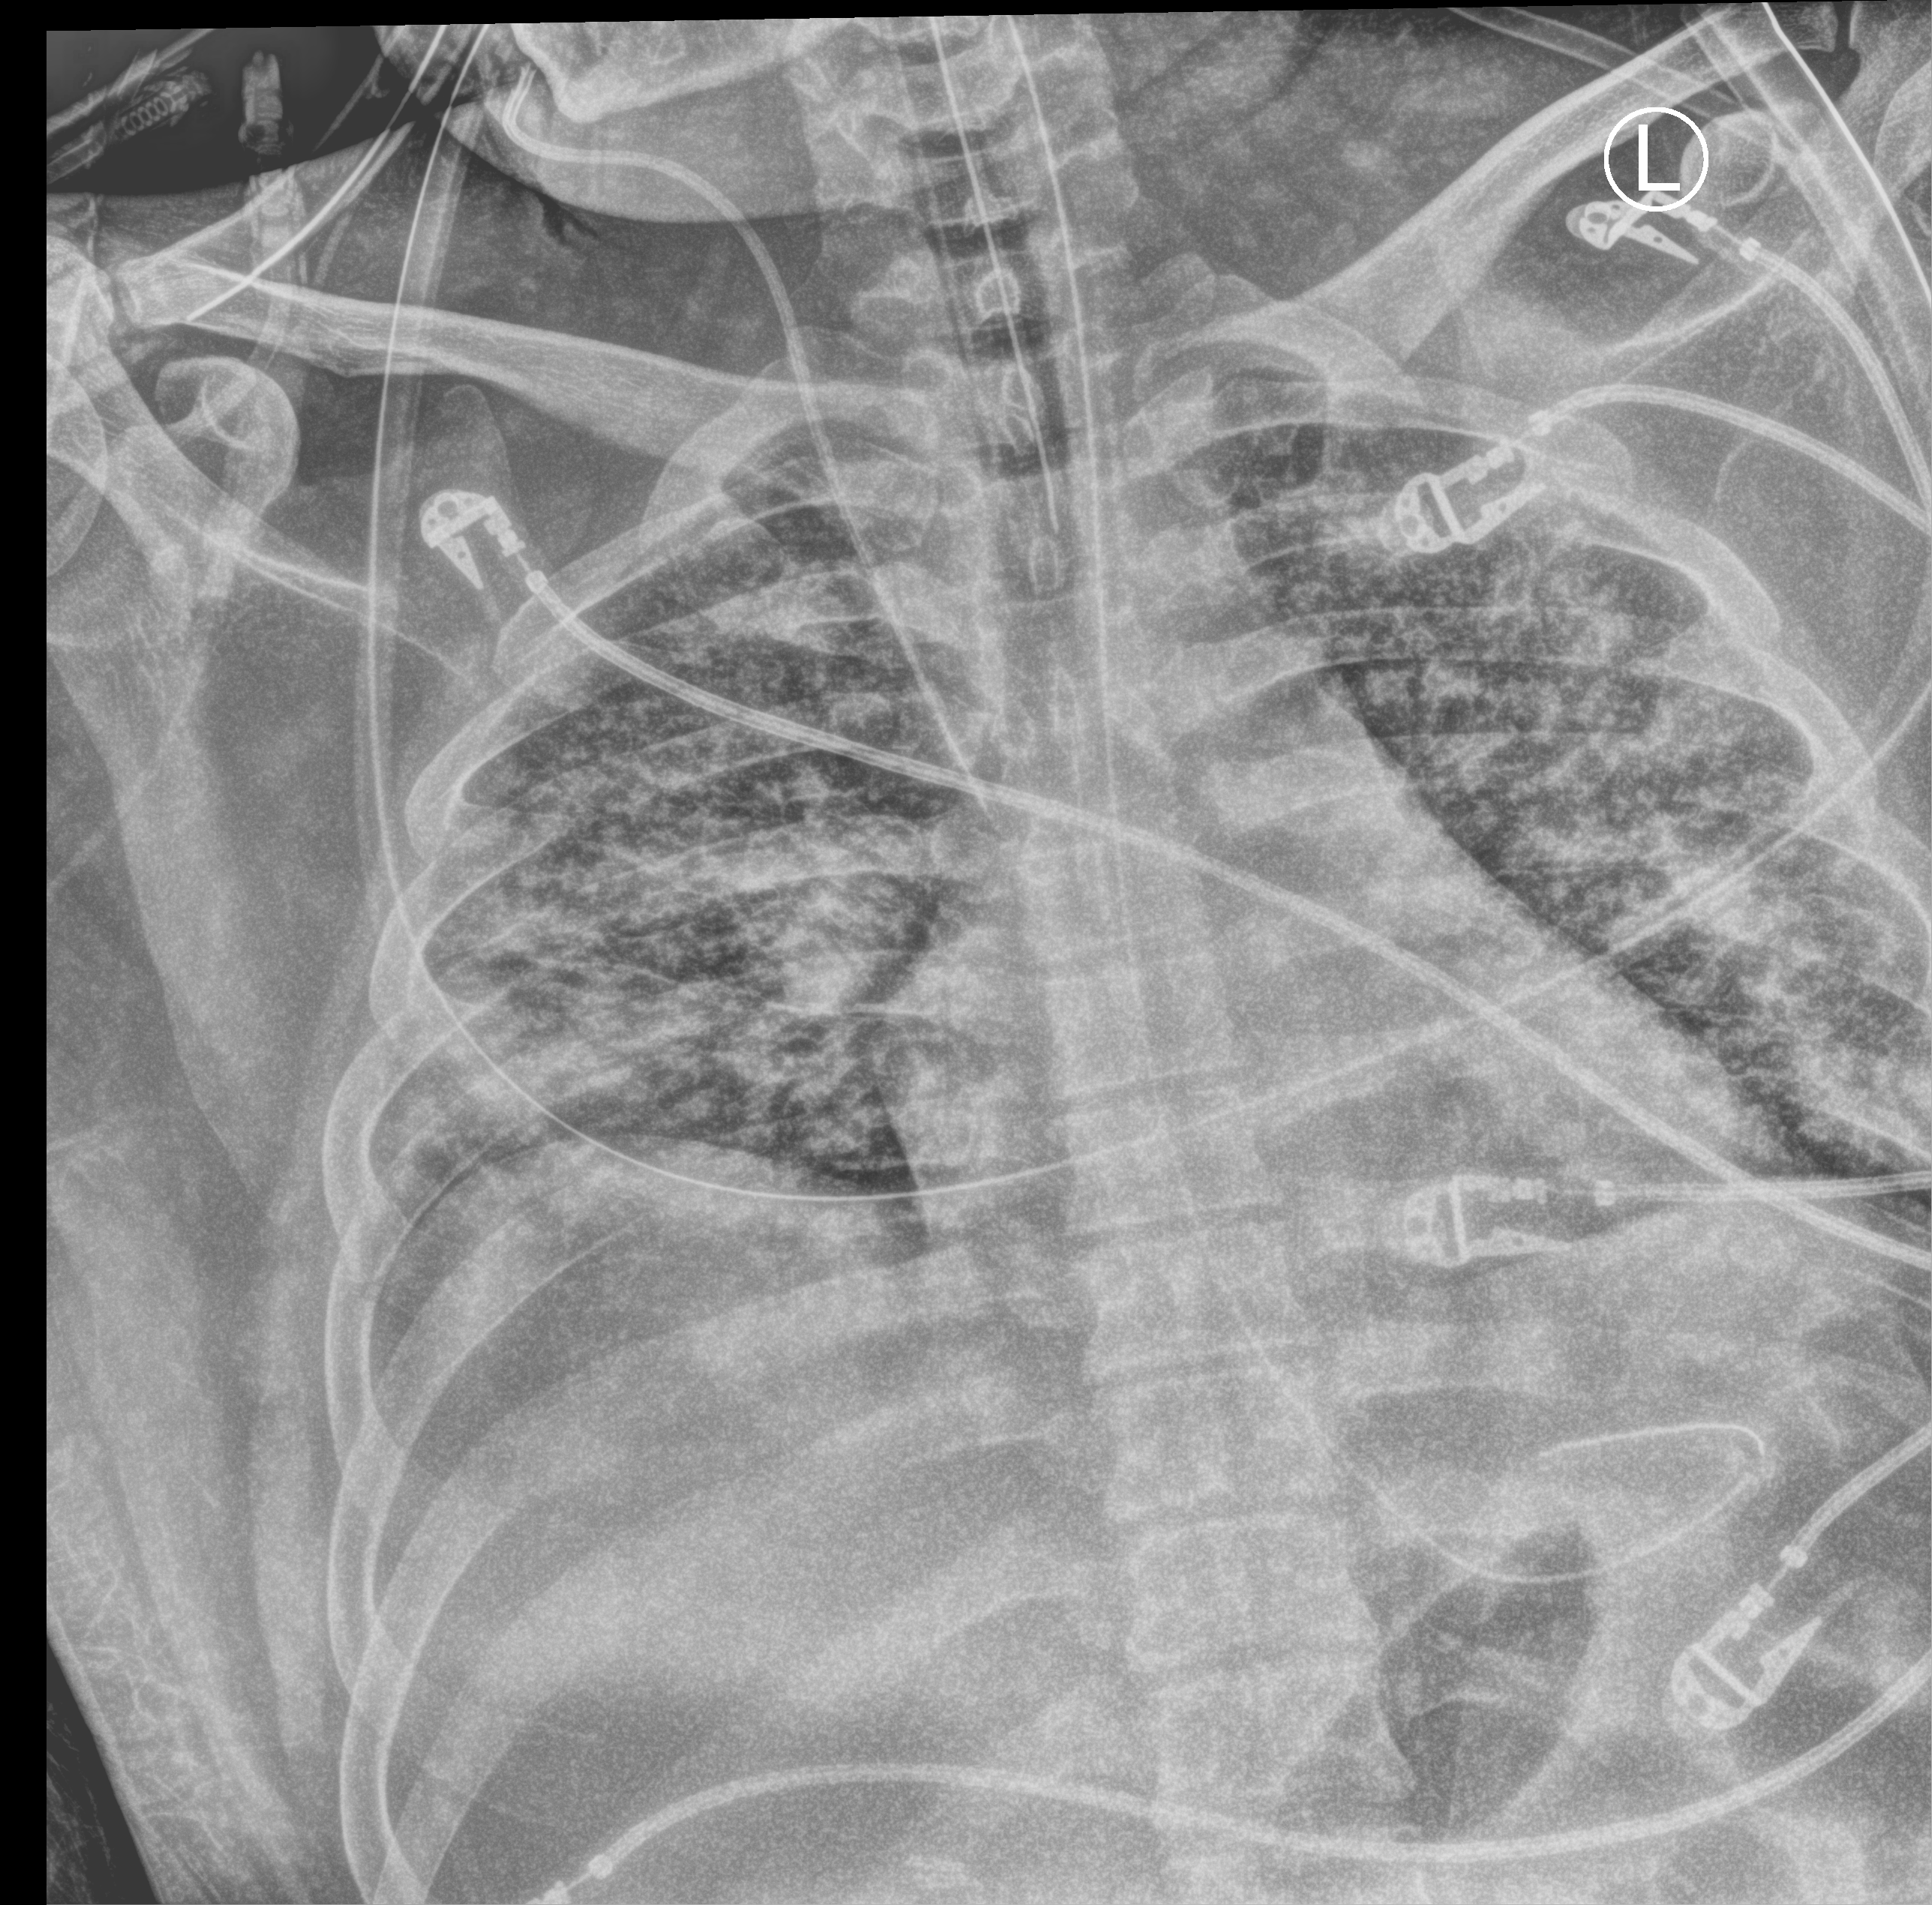
Bedside chest radiograph (computed radiography), anteroposterior (AP) projection. Male patient hospitalised with COVID-19, age 18–59 years.
From the hospital-stay record, not from the radiograph (when in the stay this image was taken is not recorded): chronic kidney disease (admission record): no; admitted to intensive care during this hospital stay: yes; mechanically ventilated during this hospital stay: yes.